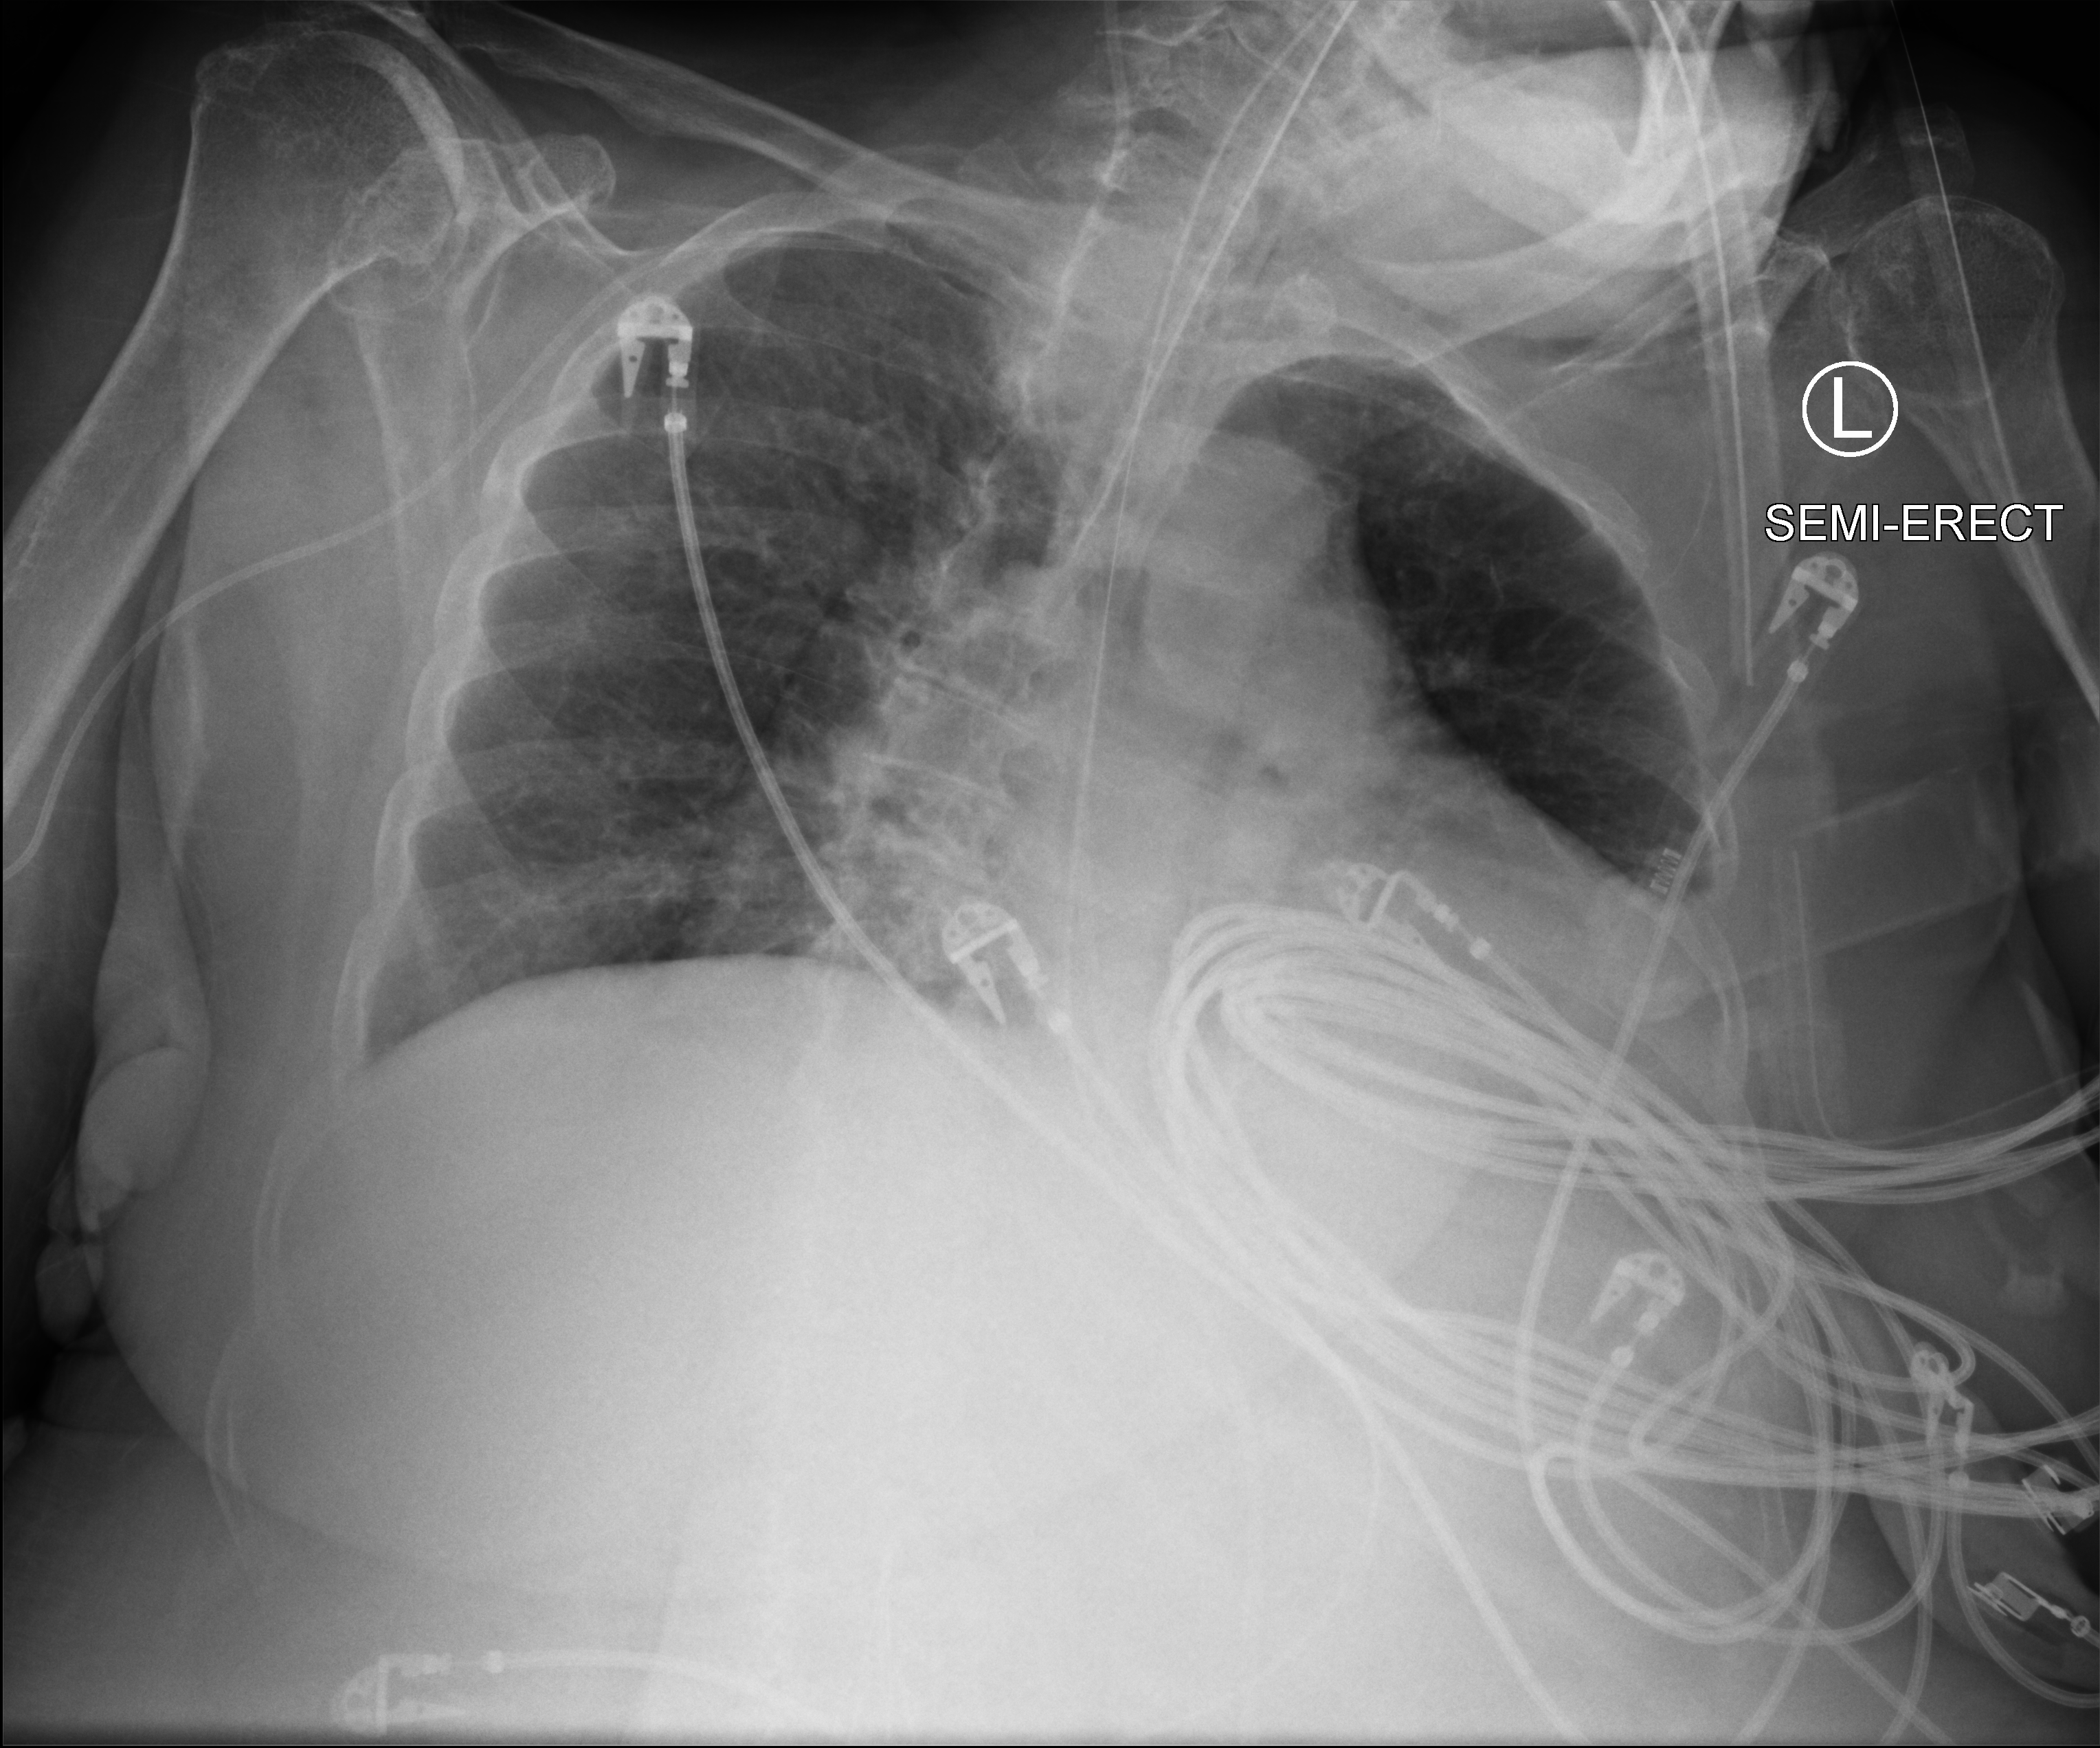
Portable chest radiograph, anteroposterior (AP) projection. Female patient hospitalised with COVID-19, age 75–90 years.
Admission-level facts for this patient (not findings on this image; timing relative to this image not recorded):
- admitted to intensive care during this hospital stay: yes
- hypertension (admission record): yes
- other chronic lung disease (admission record): no